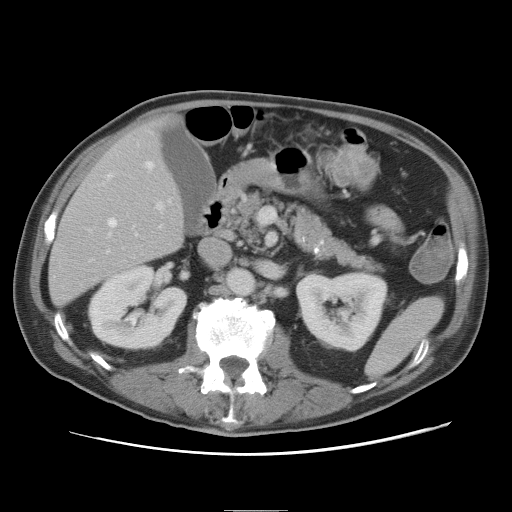
Contrast-enhanced abdominal CT, one axial slice; slice 33 of 89 in the series (ordered by position); 120 kVp; intravenous contrast given; soft-tissue window (W 400 / L 40 HU); 5 mm slice thickness; 512 × 512 image matrix, field of view 375 × 375 mm. Male patient, age 69 years. From the clinical record (not read from this slice): diagnosis: colorectal cancer liver metastases, imaged before liver resection; multiple liver metastases: no; largest metastasis: 8.5 cm; disease in both lobes: no.
Structures marked on this image (outlined manually by an expert reader):
- hepatic veins: bounding box <108,161,171,235> (left, top, right, bottom; pixels)
- liver: <50,124,184,305>
- planned liver remnant (the part of the liver to remain after resection): <50,125,184,304>
- portal vein (with intrahepatic branches): <107,201,165,253>